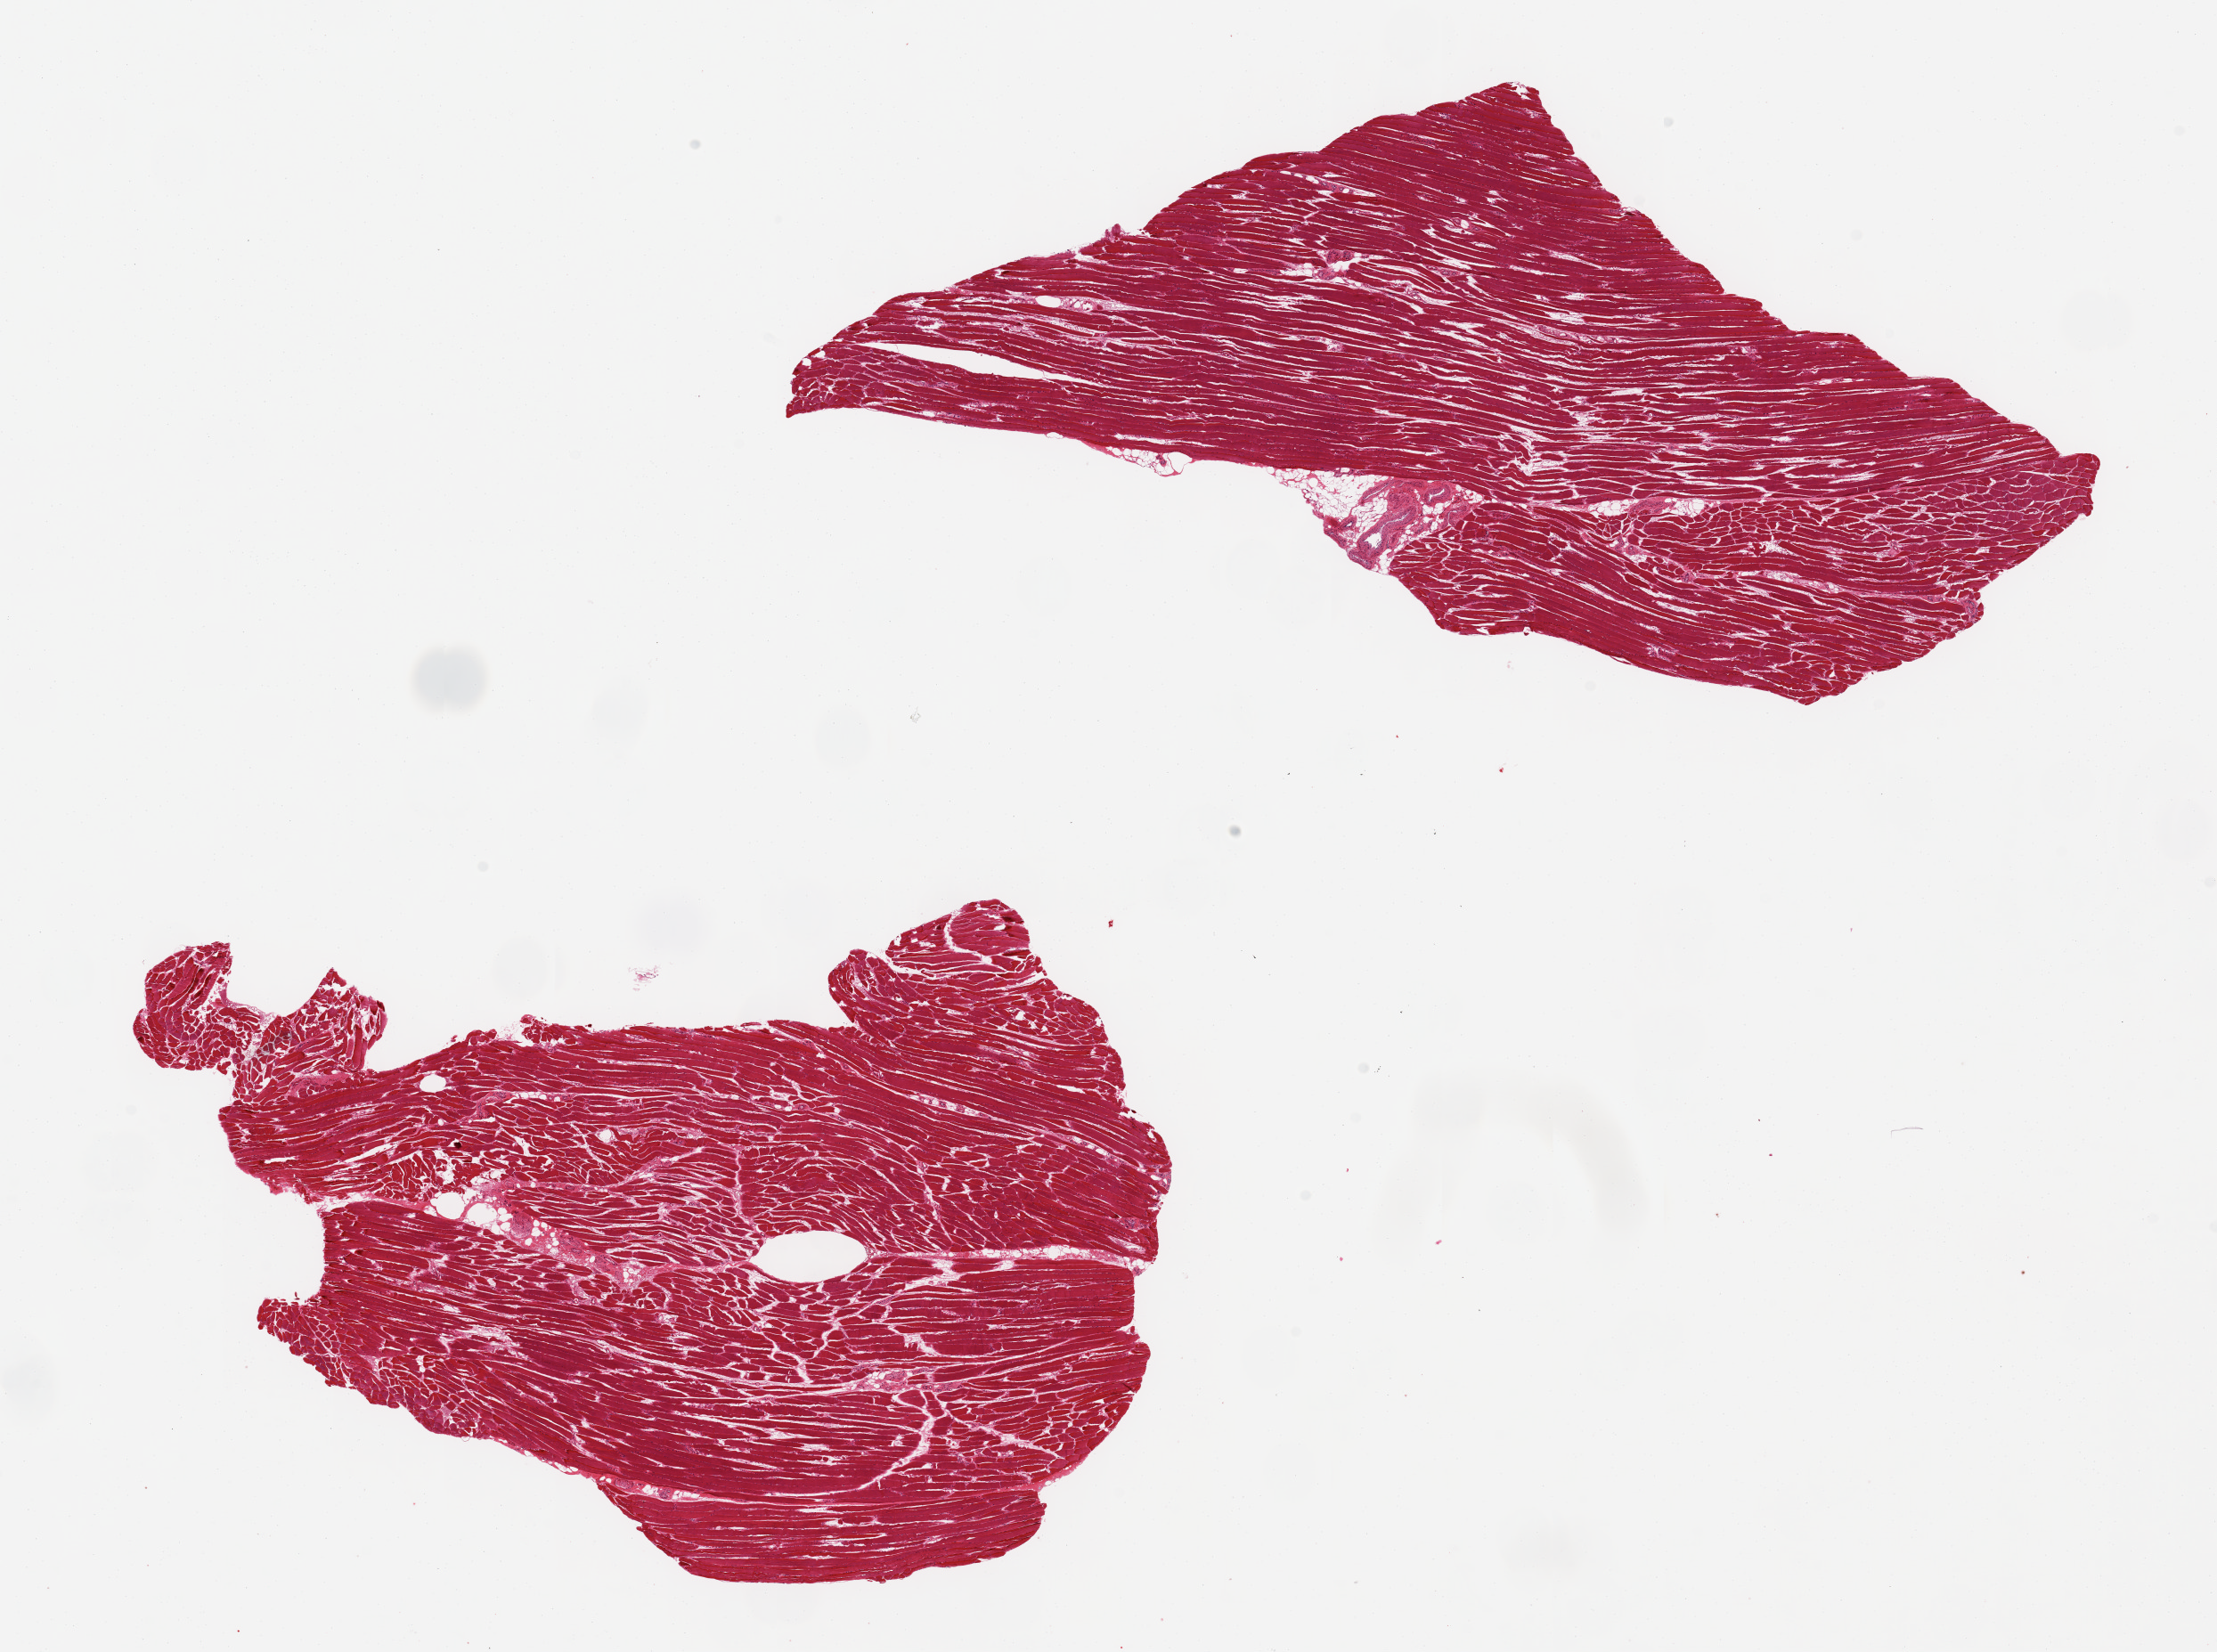
Whole-slide image, H&E stain — shown as a low-resolution overview of the whole scanned area (about 19.7 x 14.7 mm, acquisition: 20x scan), PAXgene-fixed paraffin-embedded (PFPE) section, target tissue: skeletal muscle, donor tissue sample.
Pathologist's review note for this sample: 2 9x5mm aliquots, minimal interstitial fat.